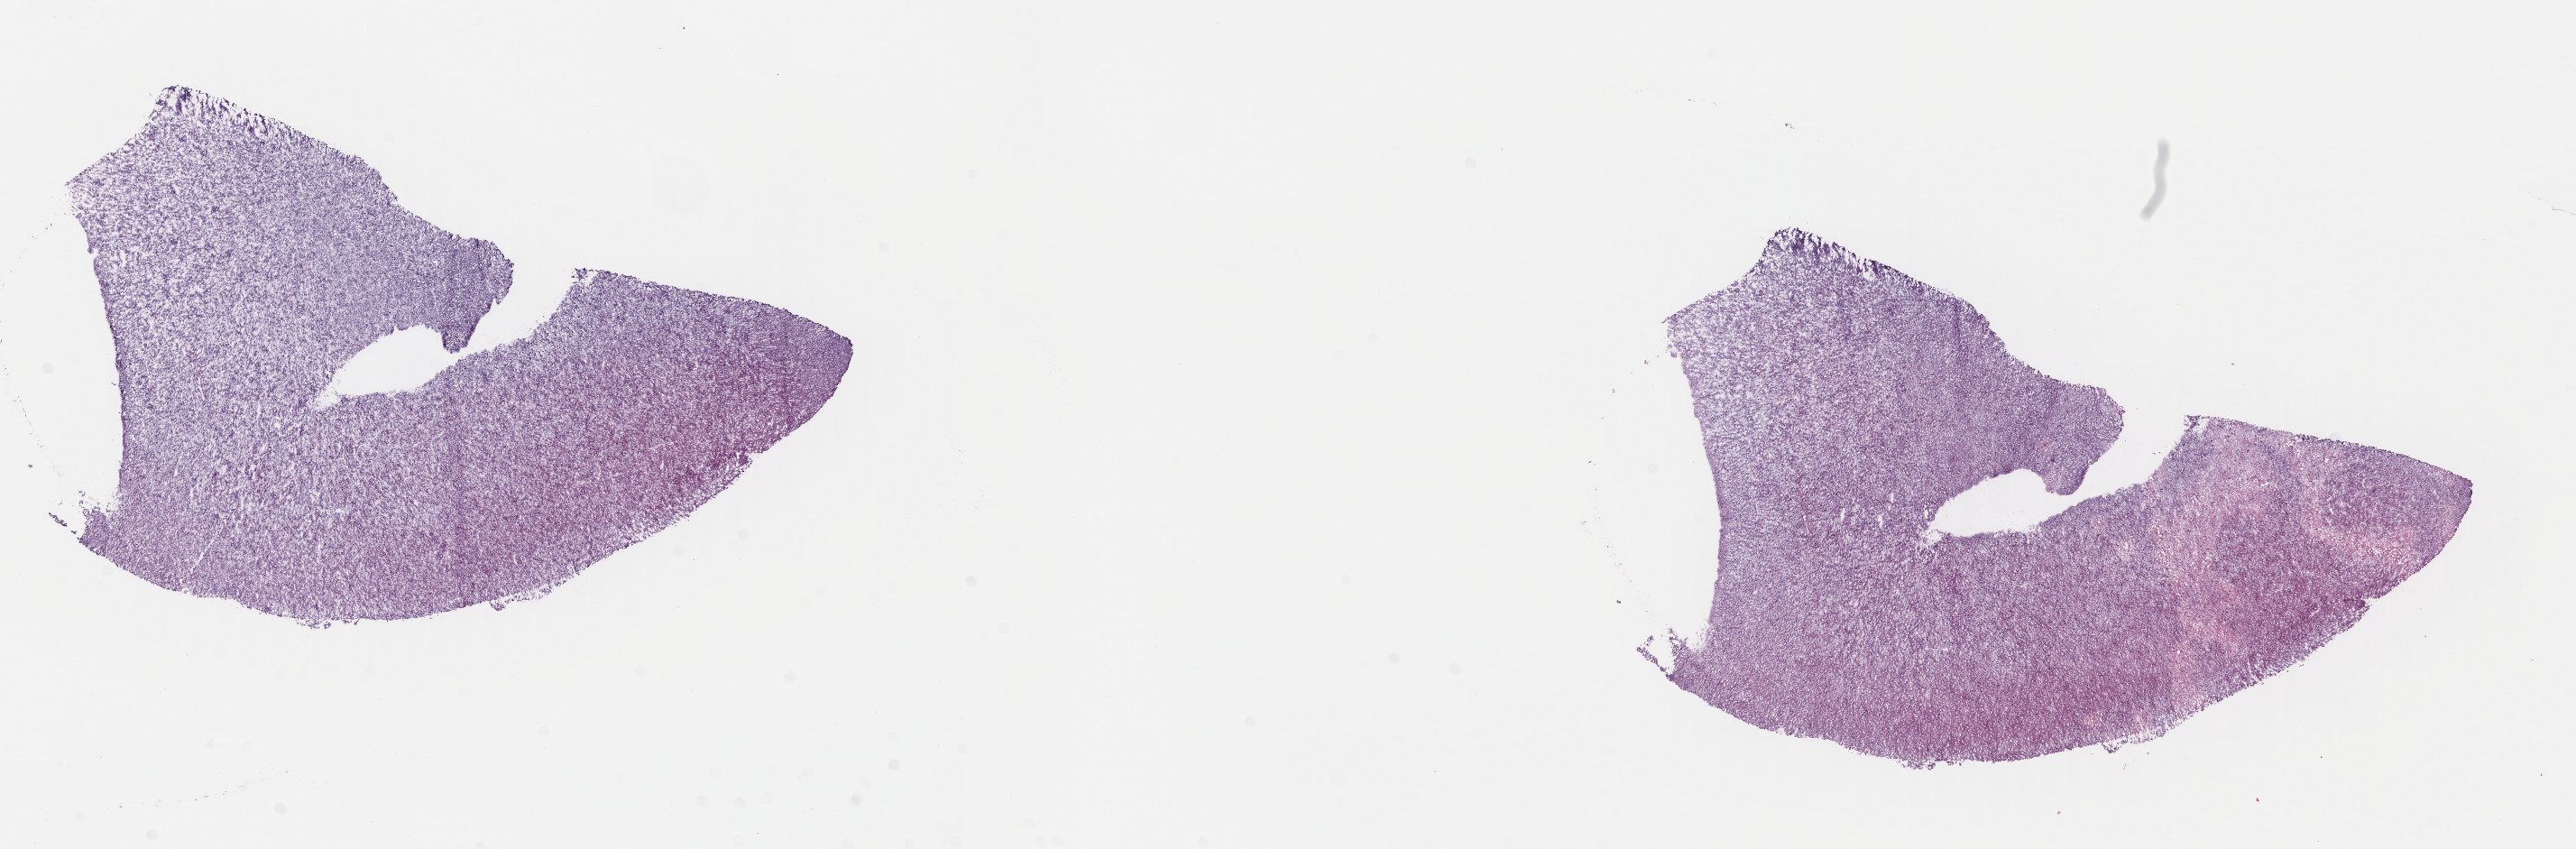
Whole-slide histology image, H&E — a low-resolution overview of the entire scanned area, about 22.4 x 7.4 mm, frozen section from the top of the tissue portion, primary tumour sample from the brain. Male, age 47 years at initial diagnosis.
Histologic diagnosis: Mixed glioma.